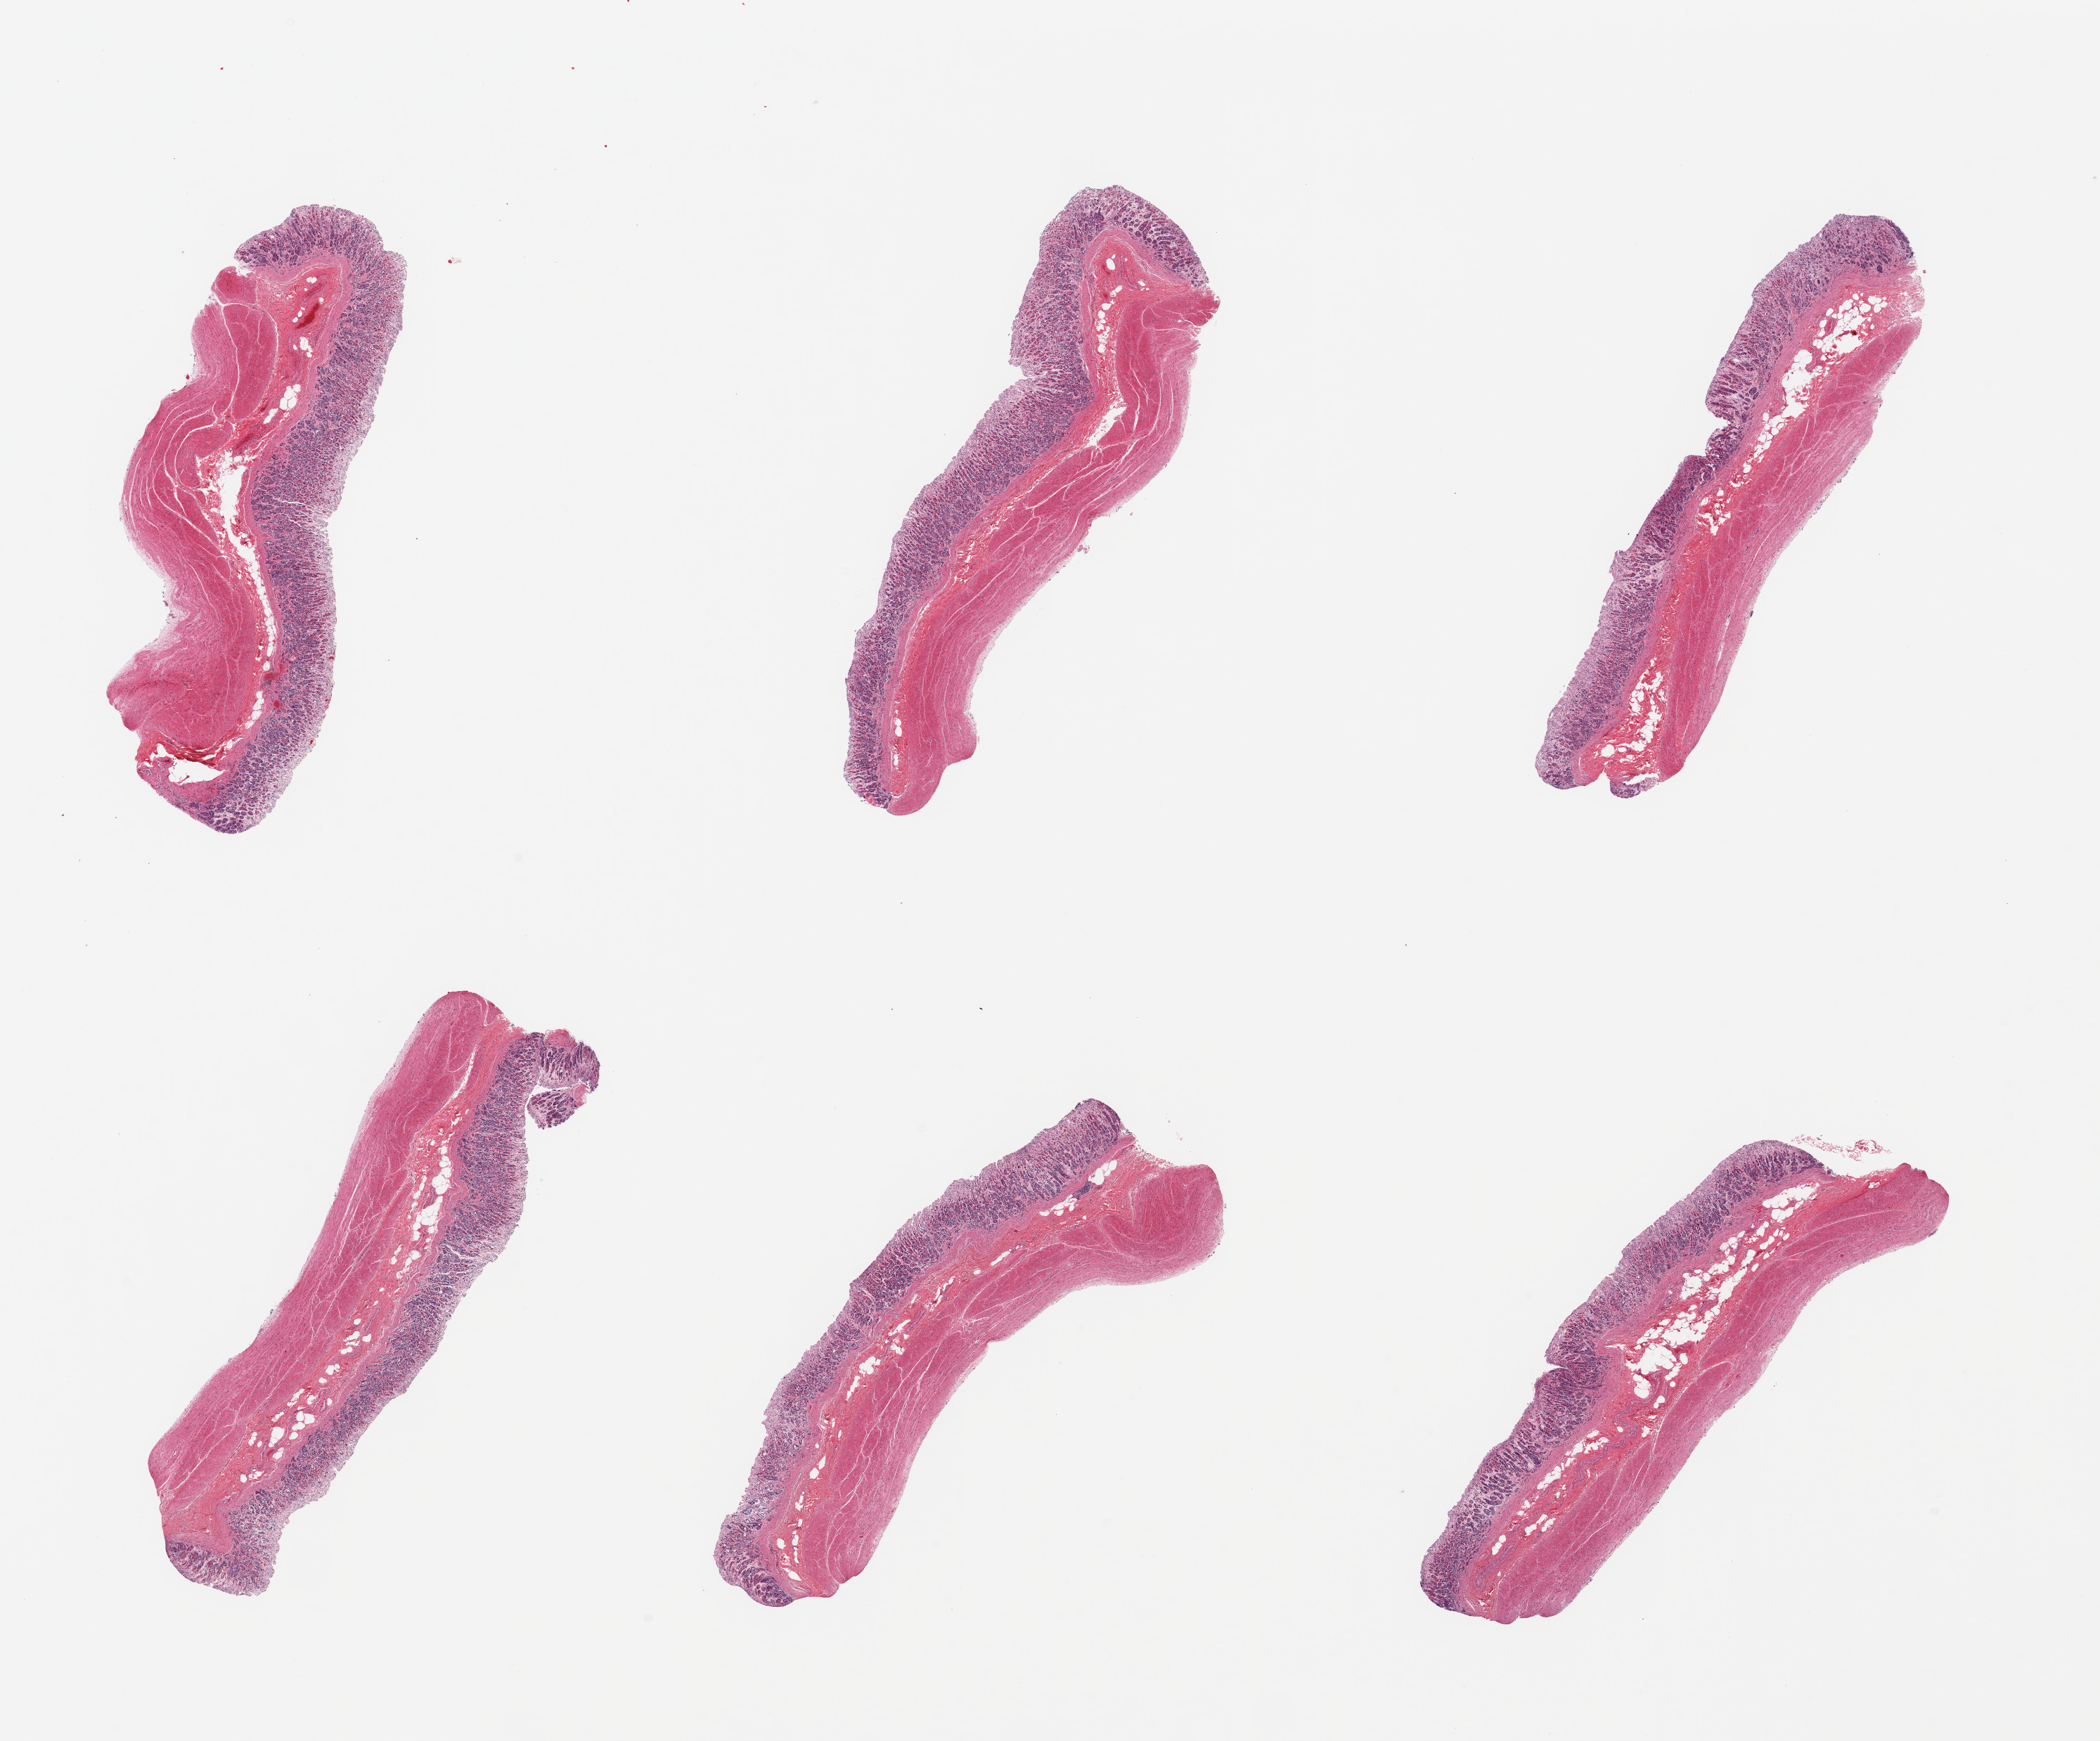
Hematoxylin and eosin (H&E) whole-slide image — shown as a low-resolution overview of the whole scanned area (about 23.6 x 19.6 mm), PAXgene-fixed, paraffin-embedded tissue, target tissue: stomach, donor tissue sample. Donor sex: female.
• reviewer comment on this tissue sample: 6 pieces; full thickness